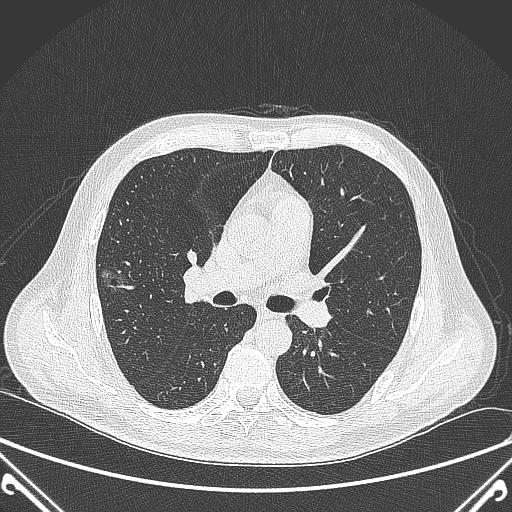
Chest CT, one axial slice. Slice 220 of 360 in the series (ordered by position). 120 kVp. Lung window (W 1500 / L -600 HU). 1 mm slice thickness. 512 × 512 image matrix, field of view 380 × 380 mm. Patient: male, 64 years. Case-level facts recorded for this patient, not image findings: clinical TNM (as recorded): T1c N0 M0; histopathological grade: G2.
Structures marked on this image (rectangle marked by the reading radiologist):
- lung tumour (recorded histology: adenocarcinoma): box from (x=89, y=262) to (x=129, y=296) px